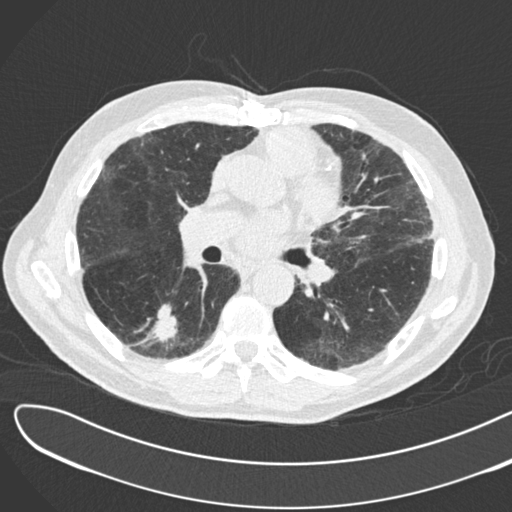
Chest CT (low-dose screening protocol), one axial image. Second annual screen. Lung window (W 1500 / L -600 HU). 2 mm slice thickness. Slice 93 of 183 in the series. 512 × 512 image matrix. Male participant, aged 72 years at enrolment. Former smoker at enrolment.
Lesion marked by an expert reader, bounding box [x1, y1, x2, y2] px = [134, 292, 193, 349]. The screening reader recorded 2 non-calcified nodules or masses ≥4 mm on this exam (right lower lobe, right lower lobe); which of them this box marks is not recorded. Lung cancer was diagnosed 46 days after this screen: squamous cell carcinoma, NOS, right lower lobe, poorly differentiated (G3), stage IB (AJCC 6th edition), 42 mm at pathology.